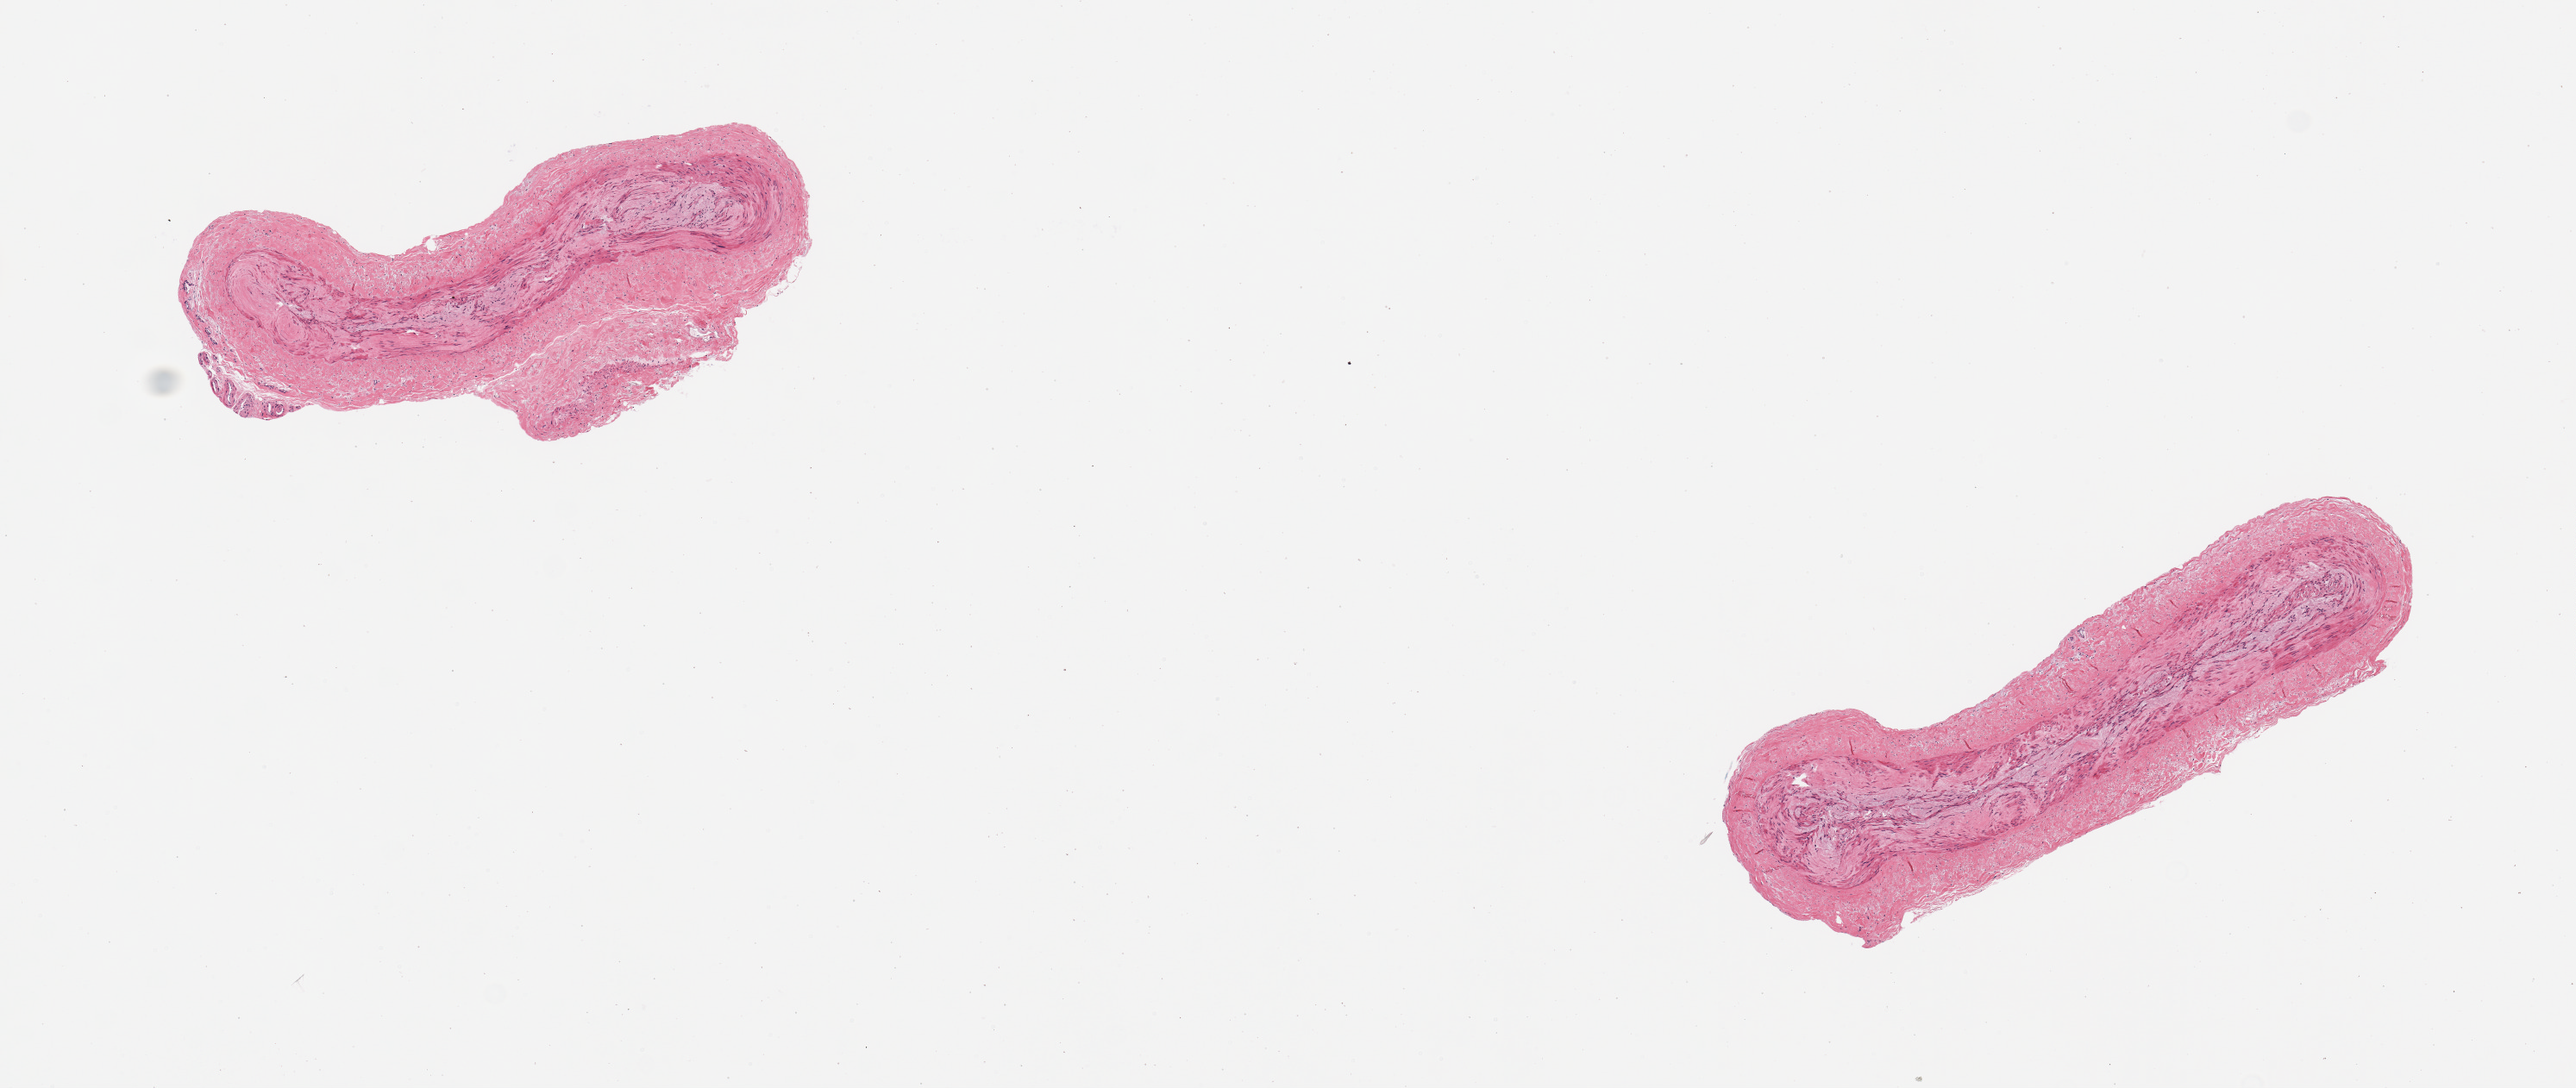
Whole-slide image, H&E stain, shown as a low-resolution overview of the whole scanned area (about 11.8 x 5.0 mm); PAXgene-fixed paraffin-embedded (PFPE) section; target tissue: tibial artery; tissue donor sample. Donor: male.
Pathologist's review note for this sample: 2 pieces. well trimmed; fibrotic wall.